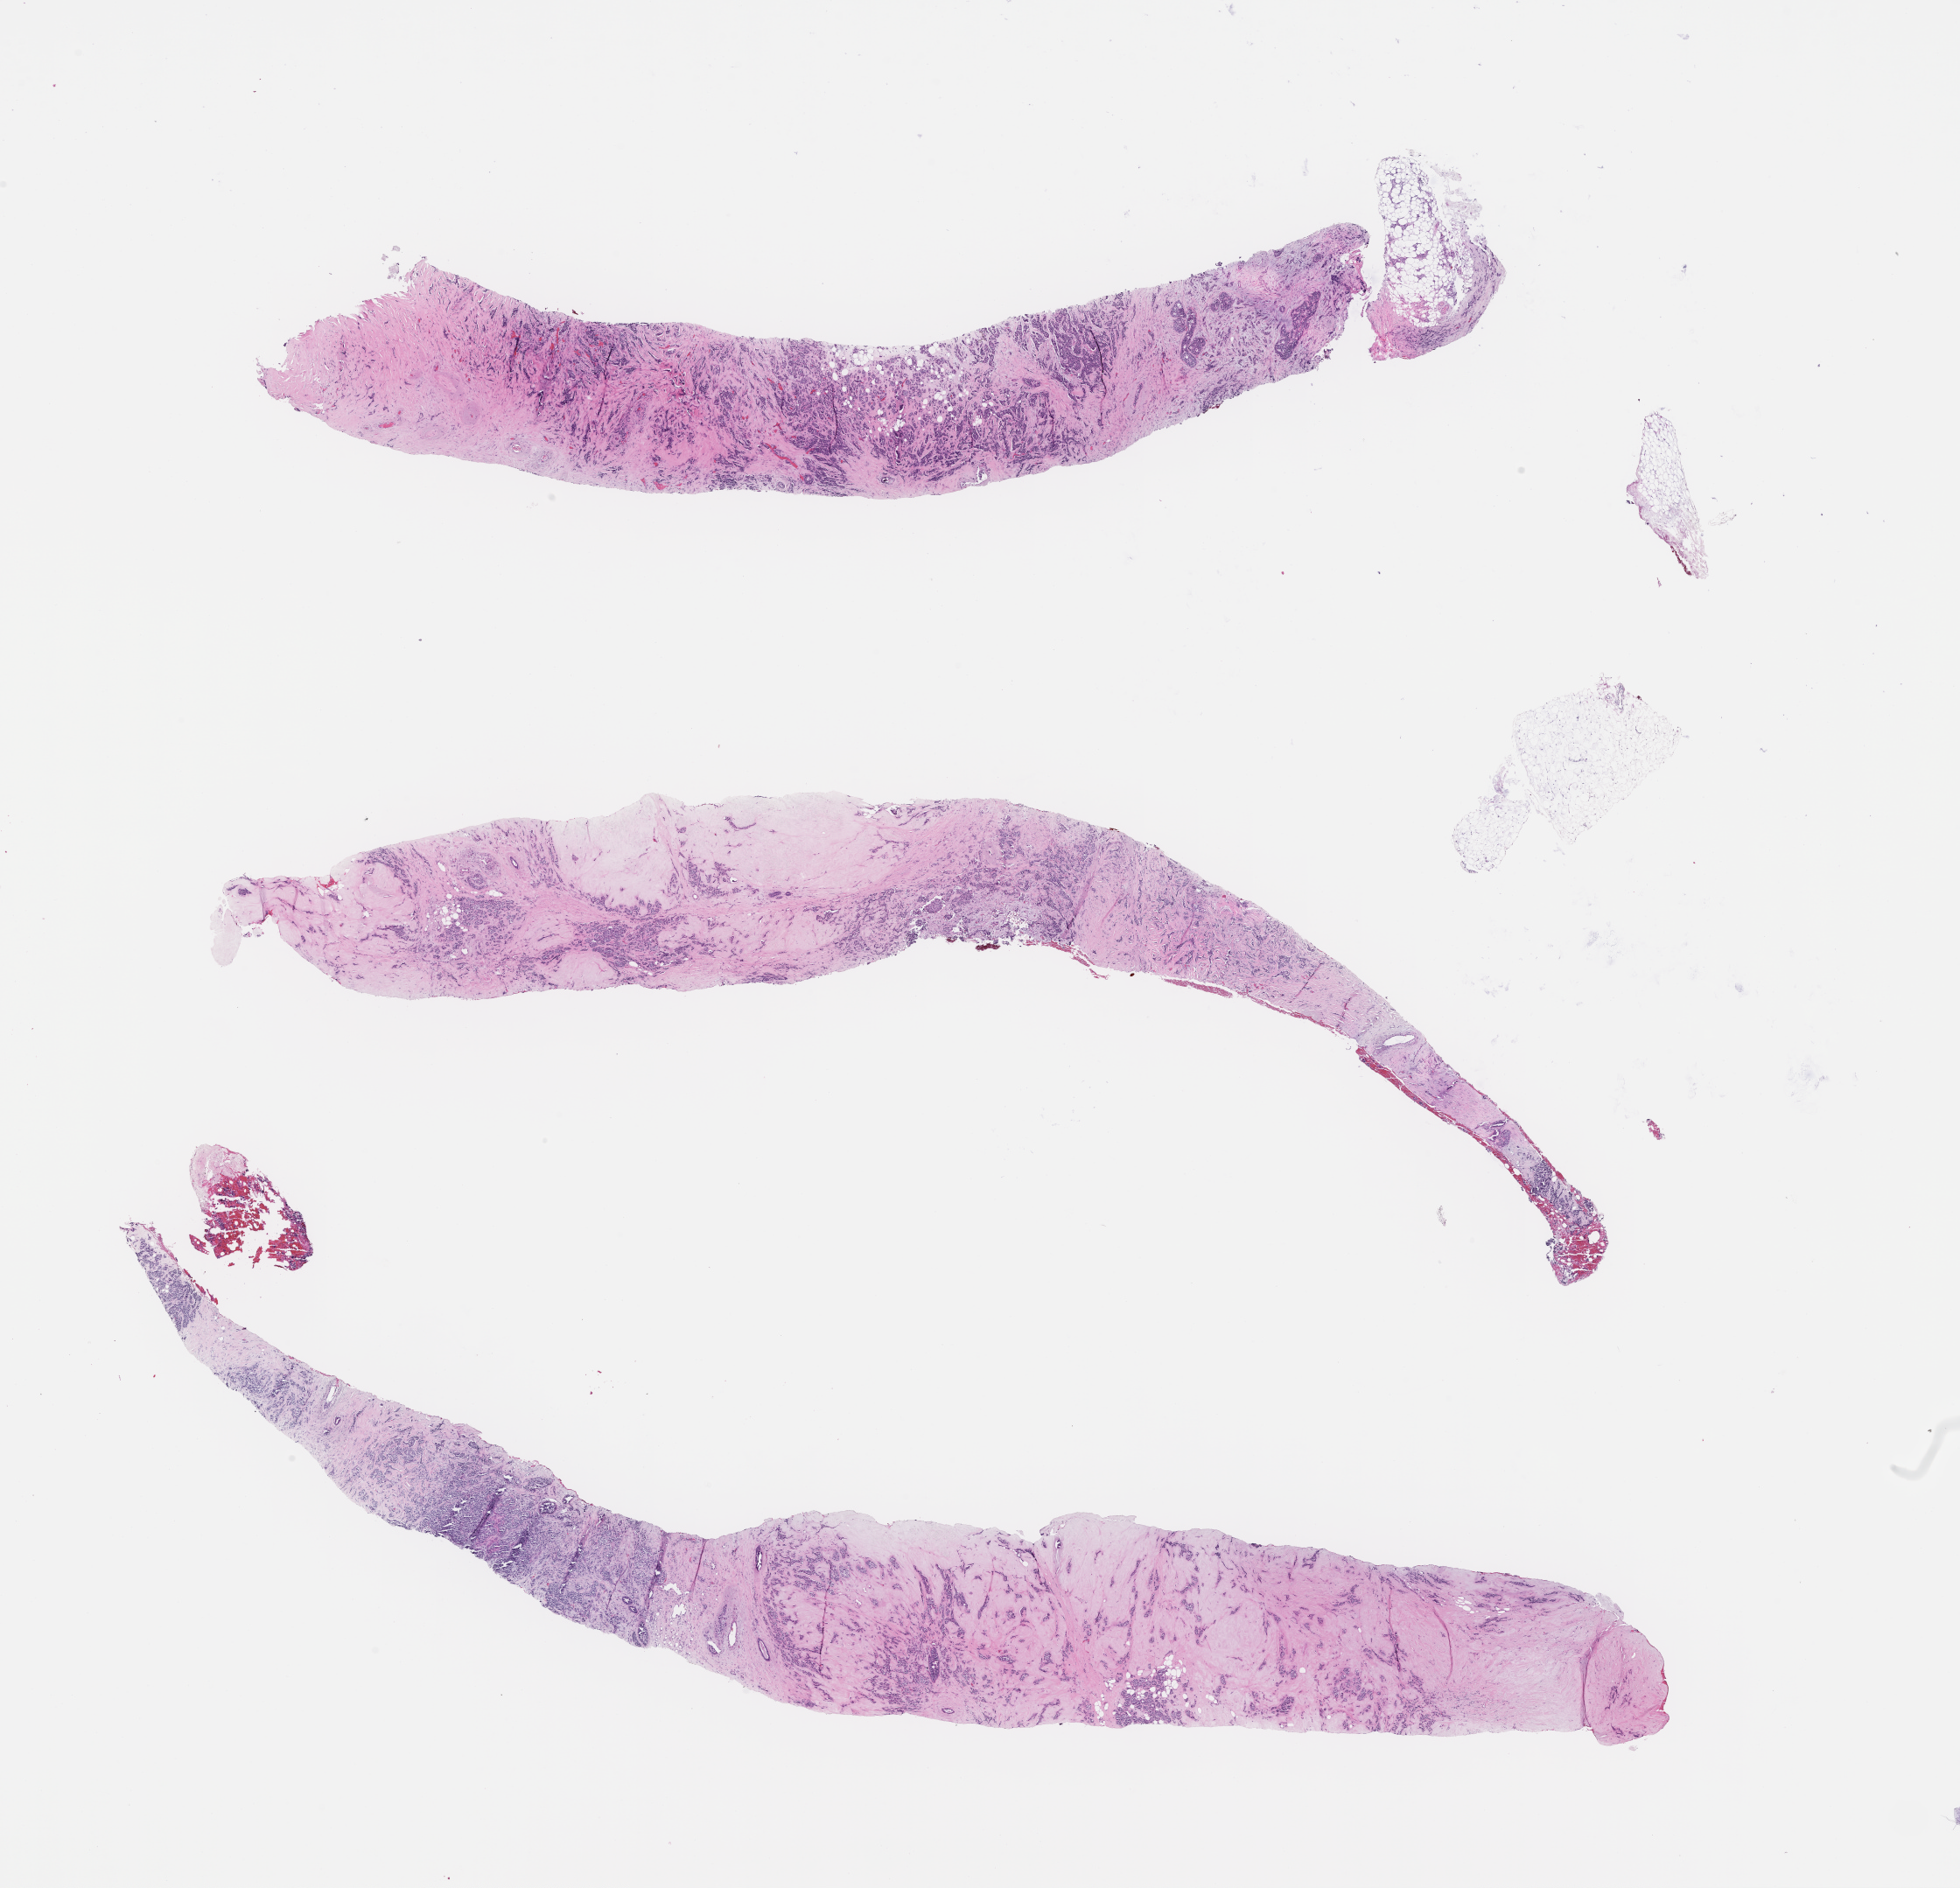
Whole-slide image, H&E stain, a low-resolution overview of the entire scanned area, about 18.1 x 17.4 mm; FFPE section; site: breast; specimen time point: archival tissue. Patient: female.
• this section: primary tumour tissue
• diagnosis: Invasive Breast Carcinoma